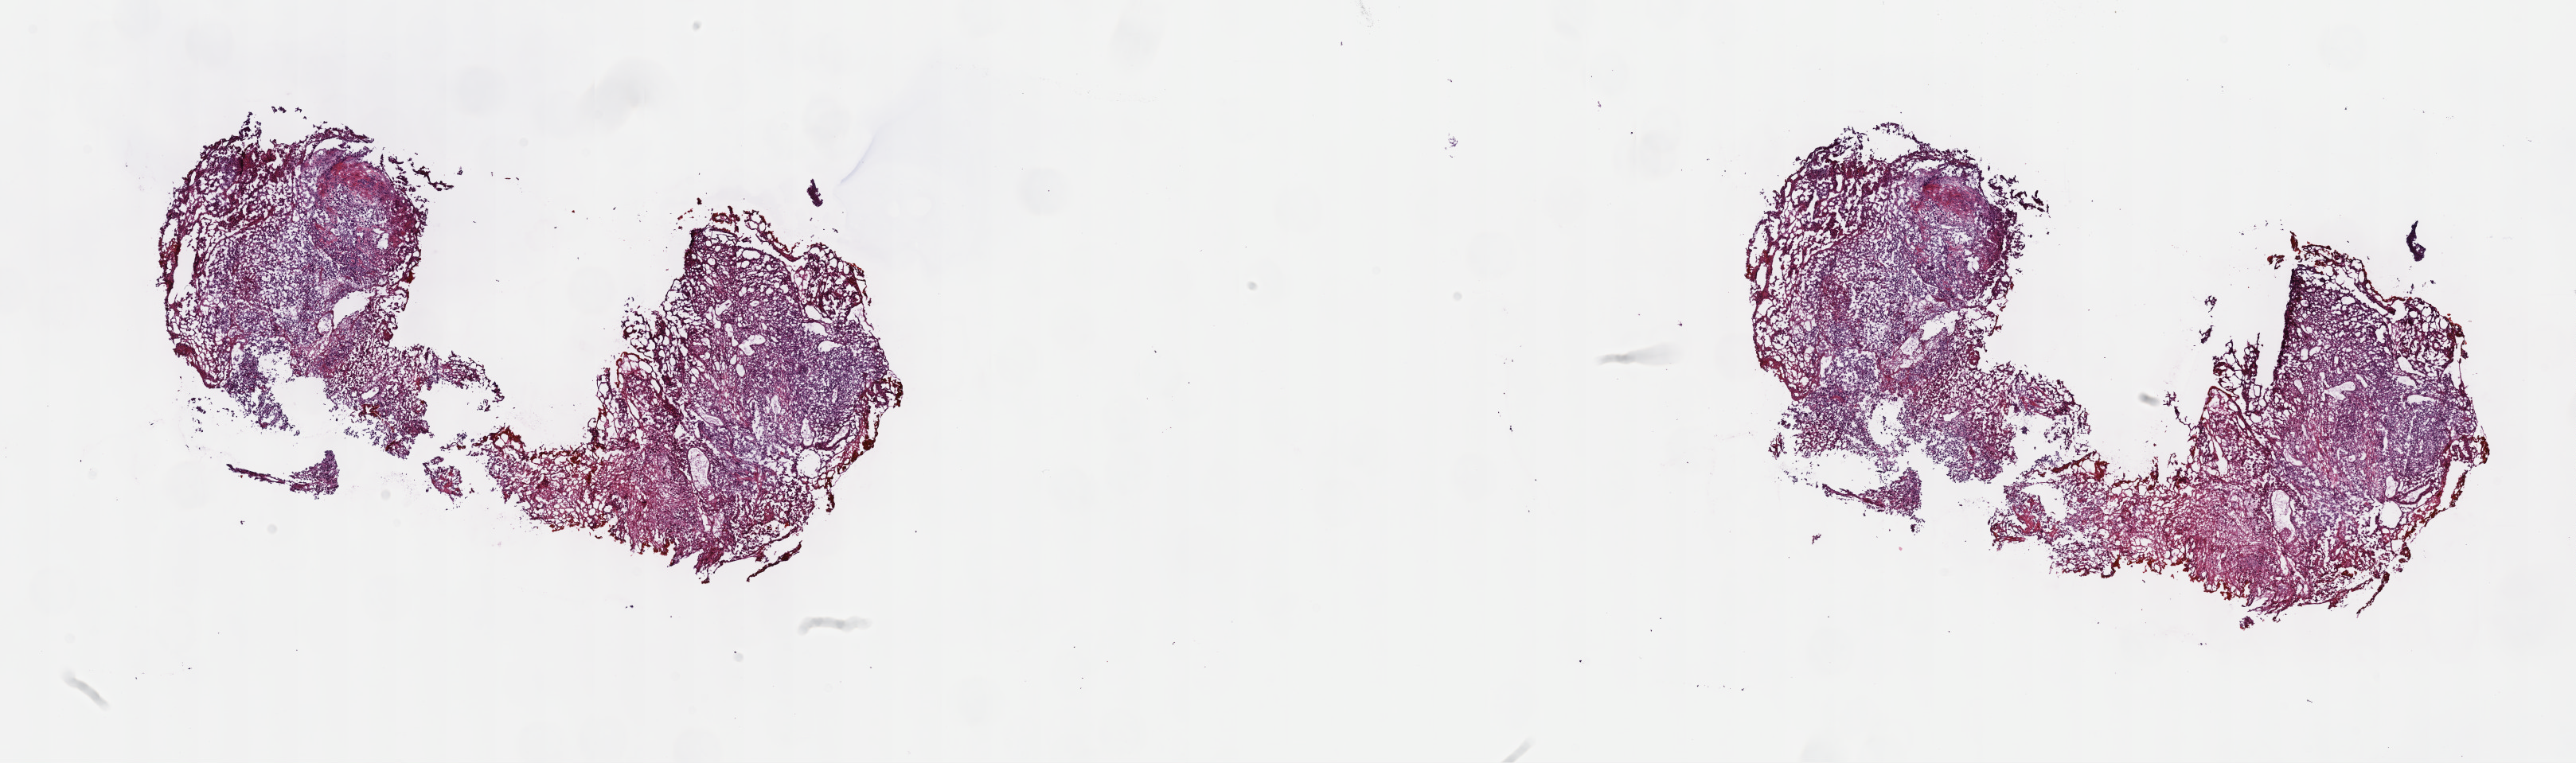
Digitized H&E tissue section (whole slide) — a low-resolution overview of the entire scanned area, about 26.2 x 7.8 mm (from a 40x scan), frozen section from the top of the tissue portion, sample: primary tumour, bladder. Male patient; age at initial diagnosis 74 years. Histologic grade: high grade. Pathologist review of this section (percent, as recorded): tumour cells 100%, tumour nuclei 70%, normal cells 0%, stromal cells 0%, necrosis 0%. Infiltration values recorded for this section: lymphocyte infiltration 0%, monocyte infiltration 0%, neutrophil infiltration 0%.
- pathologic diagnosis: Carcinoma, NOS
- AJCC pathologic stage: II (7th edition)